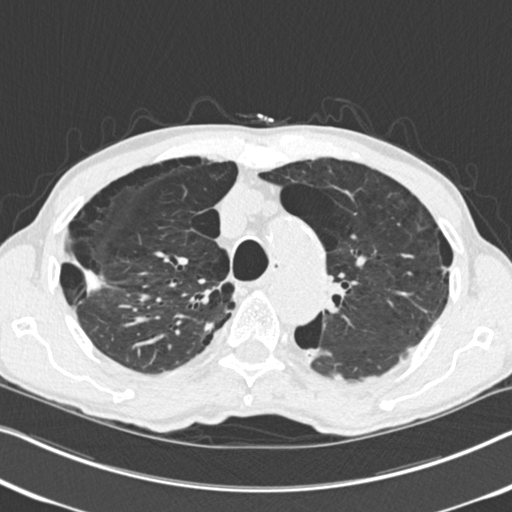
Low-dose screening chest CT, one axial slice; position 184 of 251 along the scan axis; lung window (W 1500 / L -600 HU); 2 mm slice thickness; 512 × 512 image matrix, field of view 334 × 334 mm.
Structures marked on this image (manually delineated by an expert):
- lesion 1 (tumor, upper lobe of right lung): box from (x=82, y=268) to (x=104, y=294) px